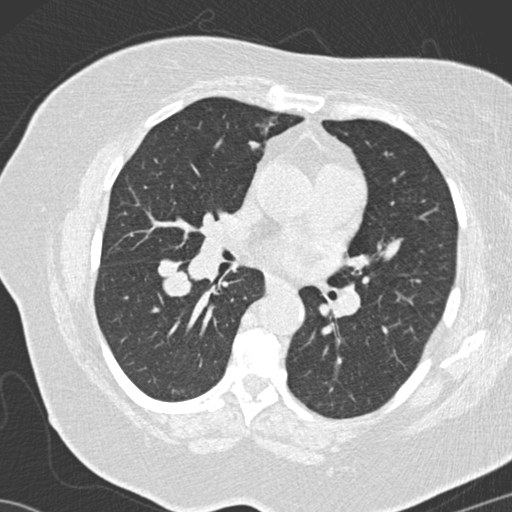
Low-dose screening chest CT, one axial slice; position 74 of 146 along the scan axis; reconstruction kernel B30f; 120 kVp; lung window (W 1500 / L -600 HU); 2 mm slice thickness; 512 × 512 image matrix.
Structures marked on this image (outlined manually by an expert reader):
- lesion 4 (tumor, lower lobe of right lung): box from (x=158, y=259) to (x=191, y=297) px